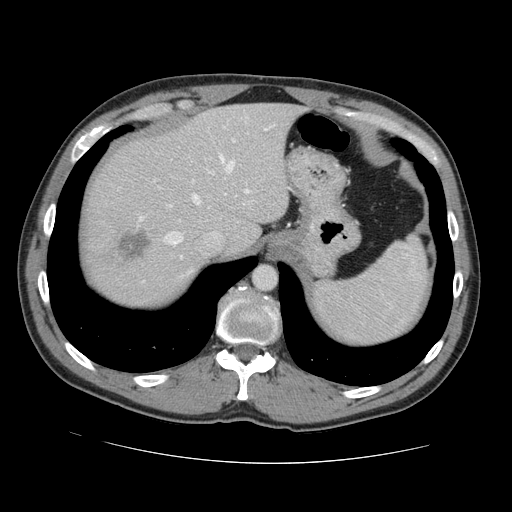
Contrast-enhanced abdominal CT, one axial slice; slice 110 of 131 in the series (ordered by position); 120 kVp; intravenous contrast given; soft-tissue window (W 400 / L 40 HU); 512 × 512 image matrix. Male patient, age 40 years. Case-level facts recorded for this patient, not image findings: diagnosis: colorectal cancer liver metastases, imaged before liver resection; multiple liver metastases: yes; largest metastasis: 2.9 cm; disease in both lobes: yes.
Annotated regions visible in this slice (manually delineated by an expert):
- hepatic veins: bounding box (x1, y1, x2, y2) in pixels: (164, 154, 234, 245)
- liver: (82, 104, 300, 304)
- planned liver remnant (the part of the liver to remain after resection): (106, 104, 300, 253)
- portal vein (with intrahepatic branches): (209, 133, 251, 194)
- liver metastasis: (118, 227, 150, 262)